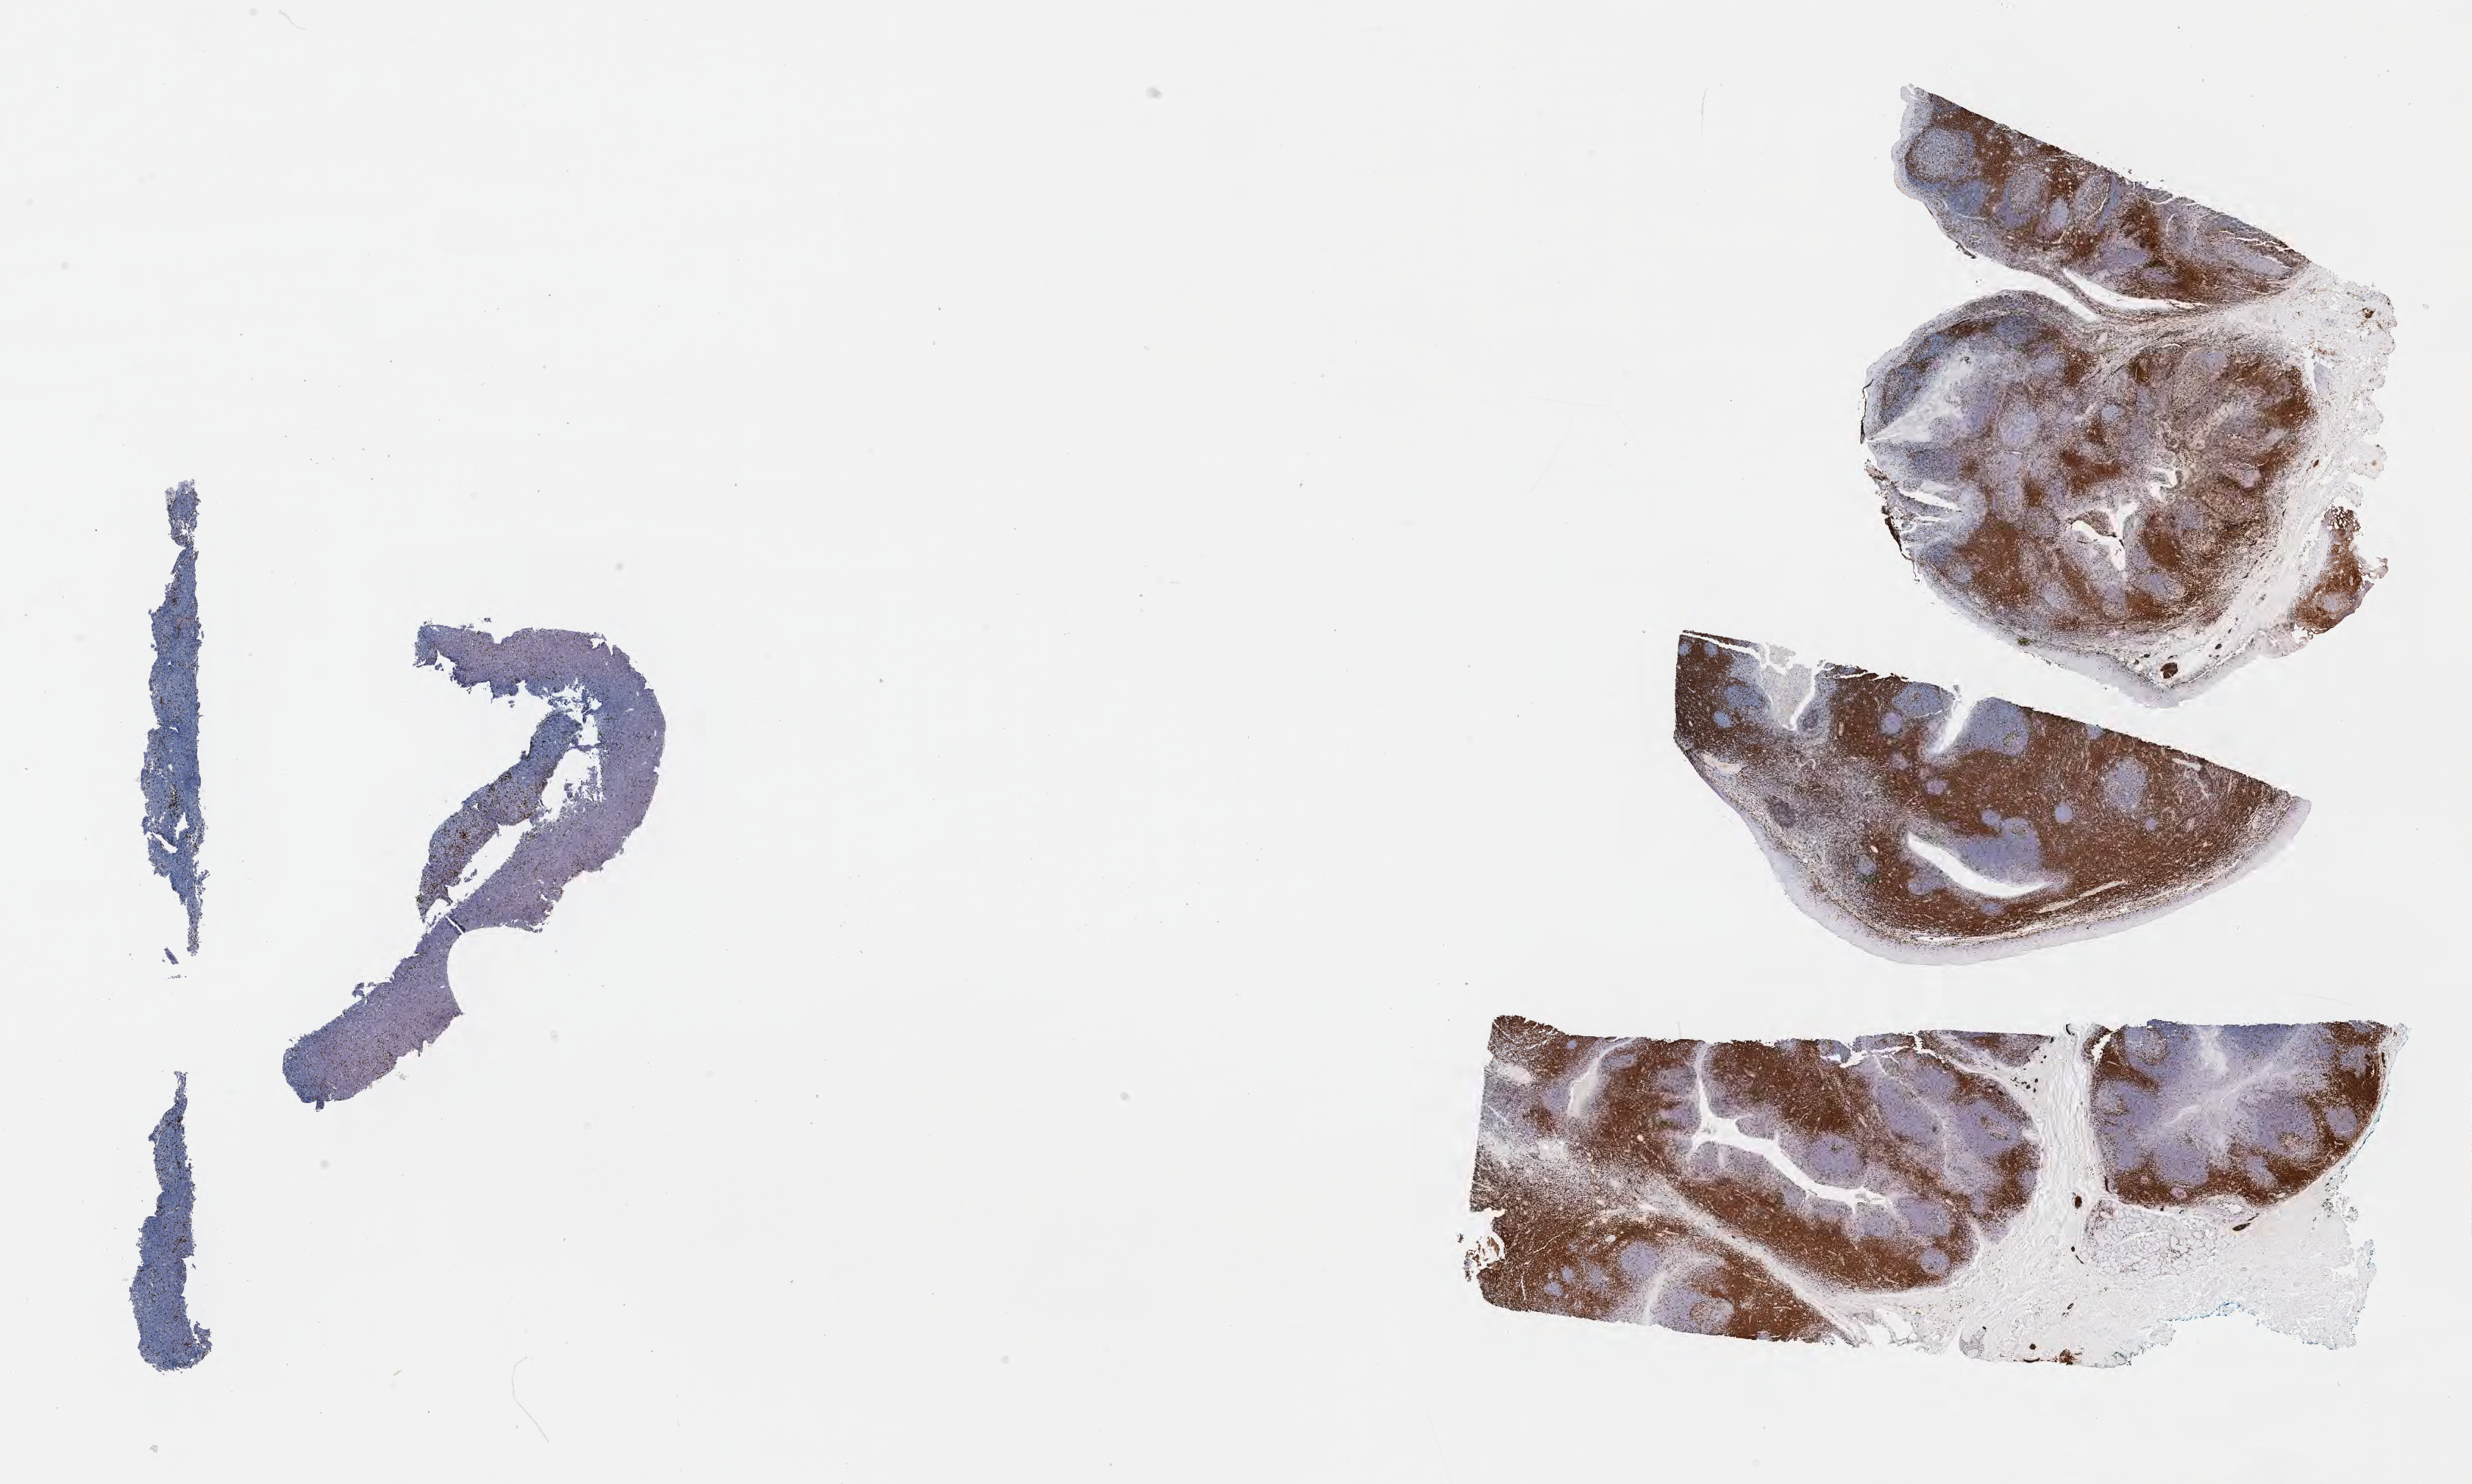
IHC for CD3, whole-slide image, a low-resolution overview of the entire scanned area, about 27.2 x 16.3 mm; tumor tissue; site: peritoneum. Patient: female, age at initial diagnosis 7 years.
* histologic diagnosis: Burkitt lymphoma, NOS